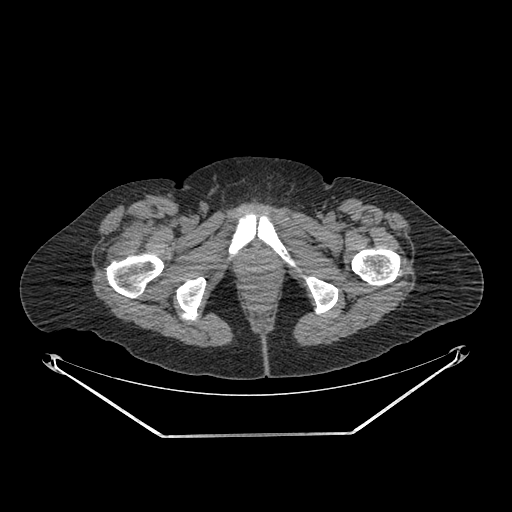
CT of an extremity soft-tissue mass (from a PET/CT study), one axial slice. Position 285 of 311 along the scan axis. Reconstruction kernel SOFT. Soft-tissue window (W 400 / L 40 HU). 512 × 512 image matrix, field of view 500 × 500 mm. Female patient. Case-level facts recorded for this patient, not image findings: histological type: pleiomorphic undifferentiated sarcoma; grade: high; site of the primary tumour: right quadricep.
Annotated regions visible in this slice (expert contour drawn on MRI and transferred to this co-registered scan by the dataset authors):
- tumour plus oedema (research contour): bounding box (x1, y1, x2, y2) in pixels: (105, 230, 156, 268)